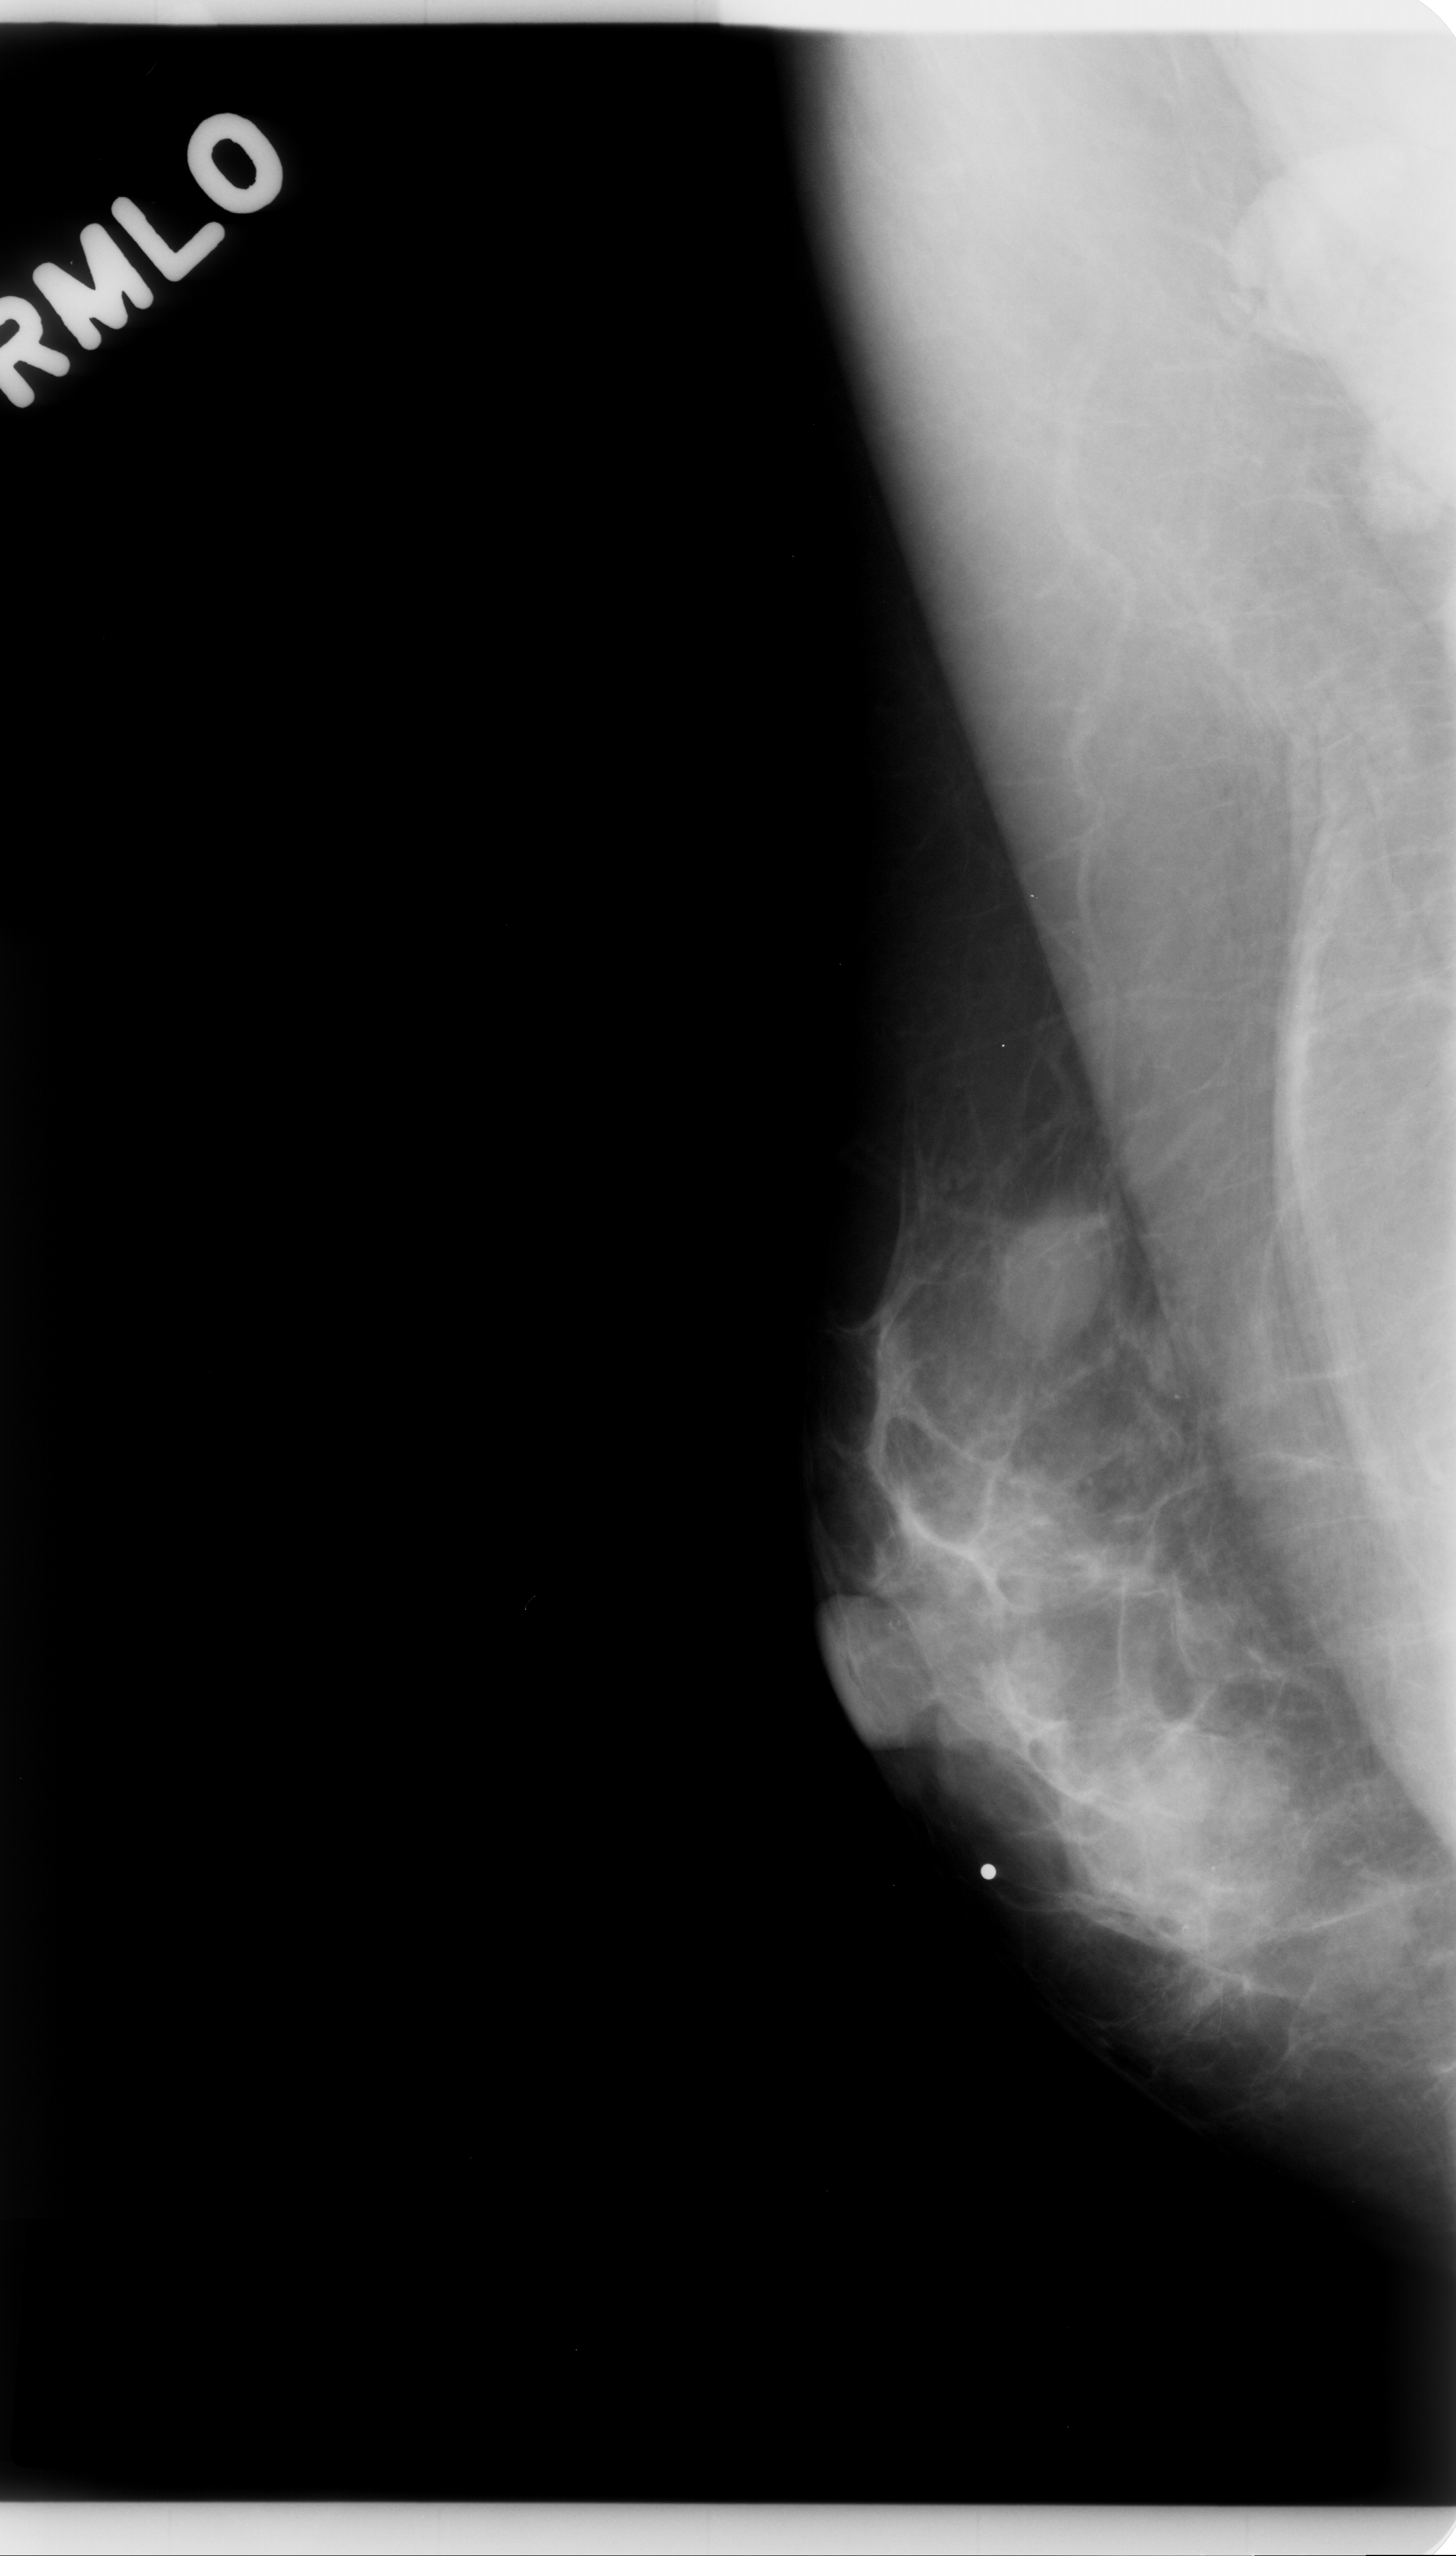
Scanned film-screen mammogram, right breast, MLO view.
- Abnormality record for this image: mass, shape oval, margins circumscribed; BI-RADS assessment category 3; pathology (as recorded): benign.